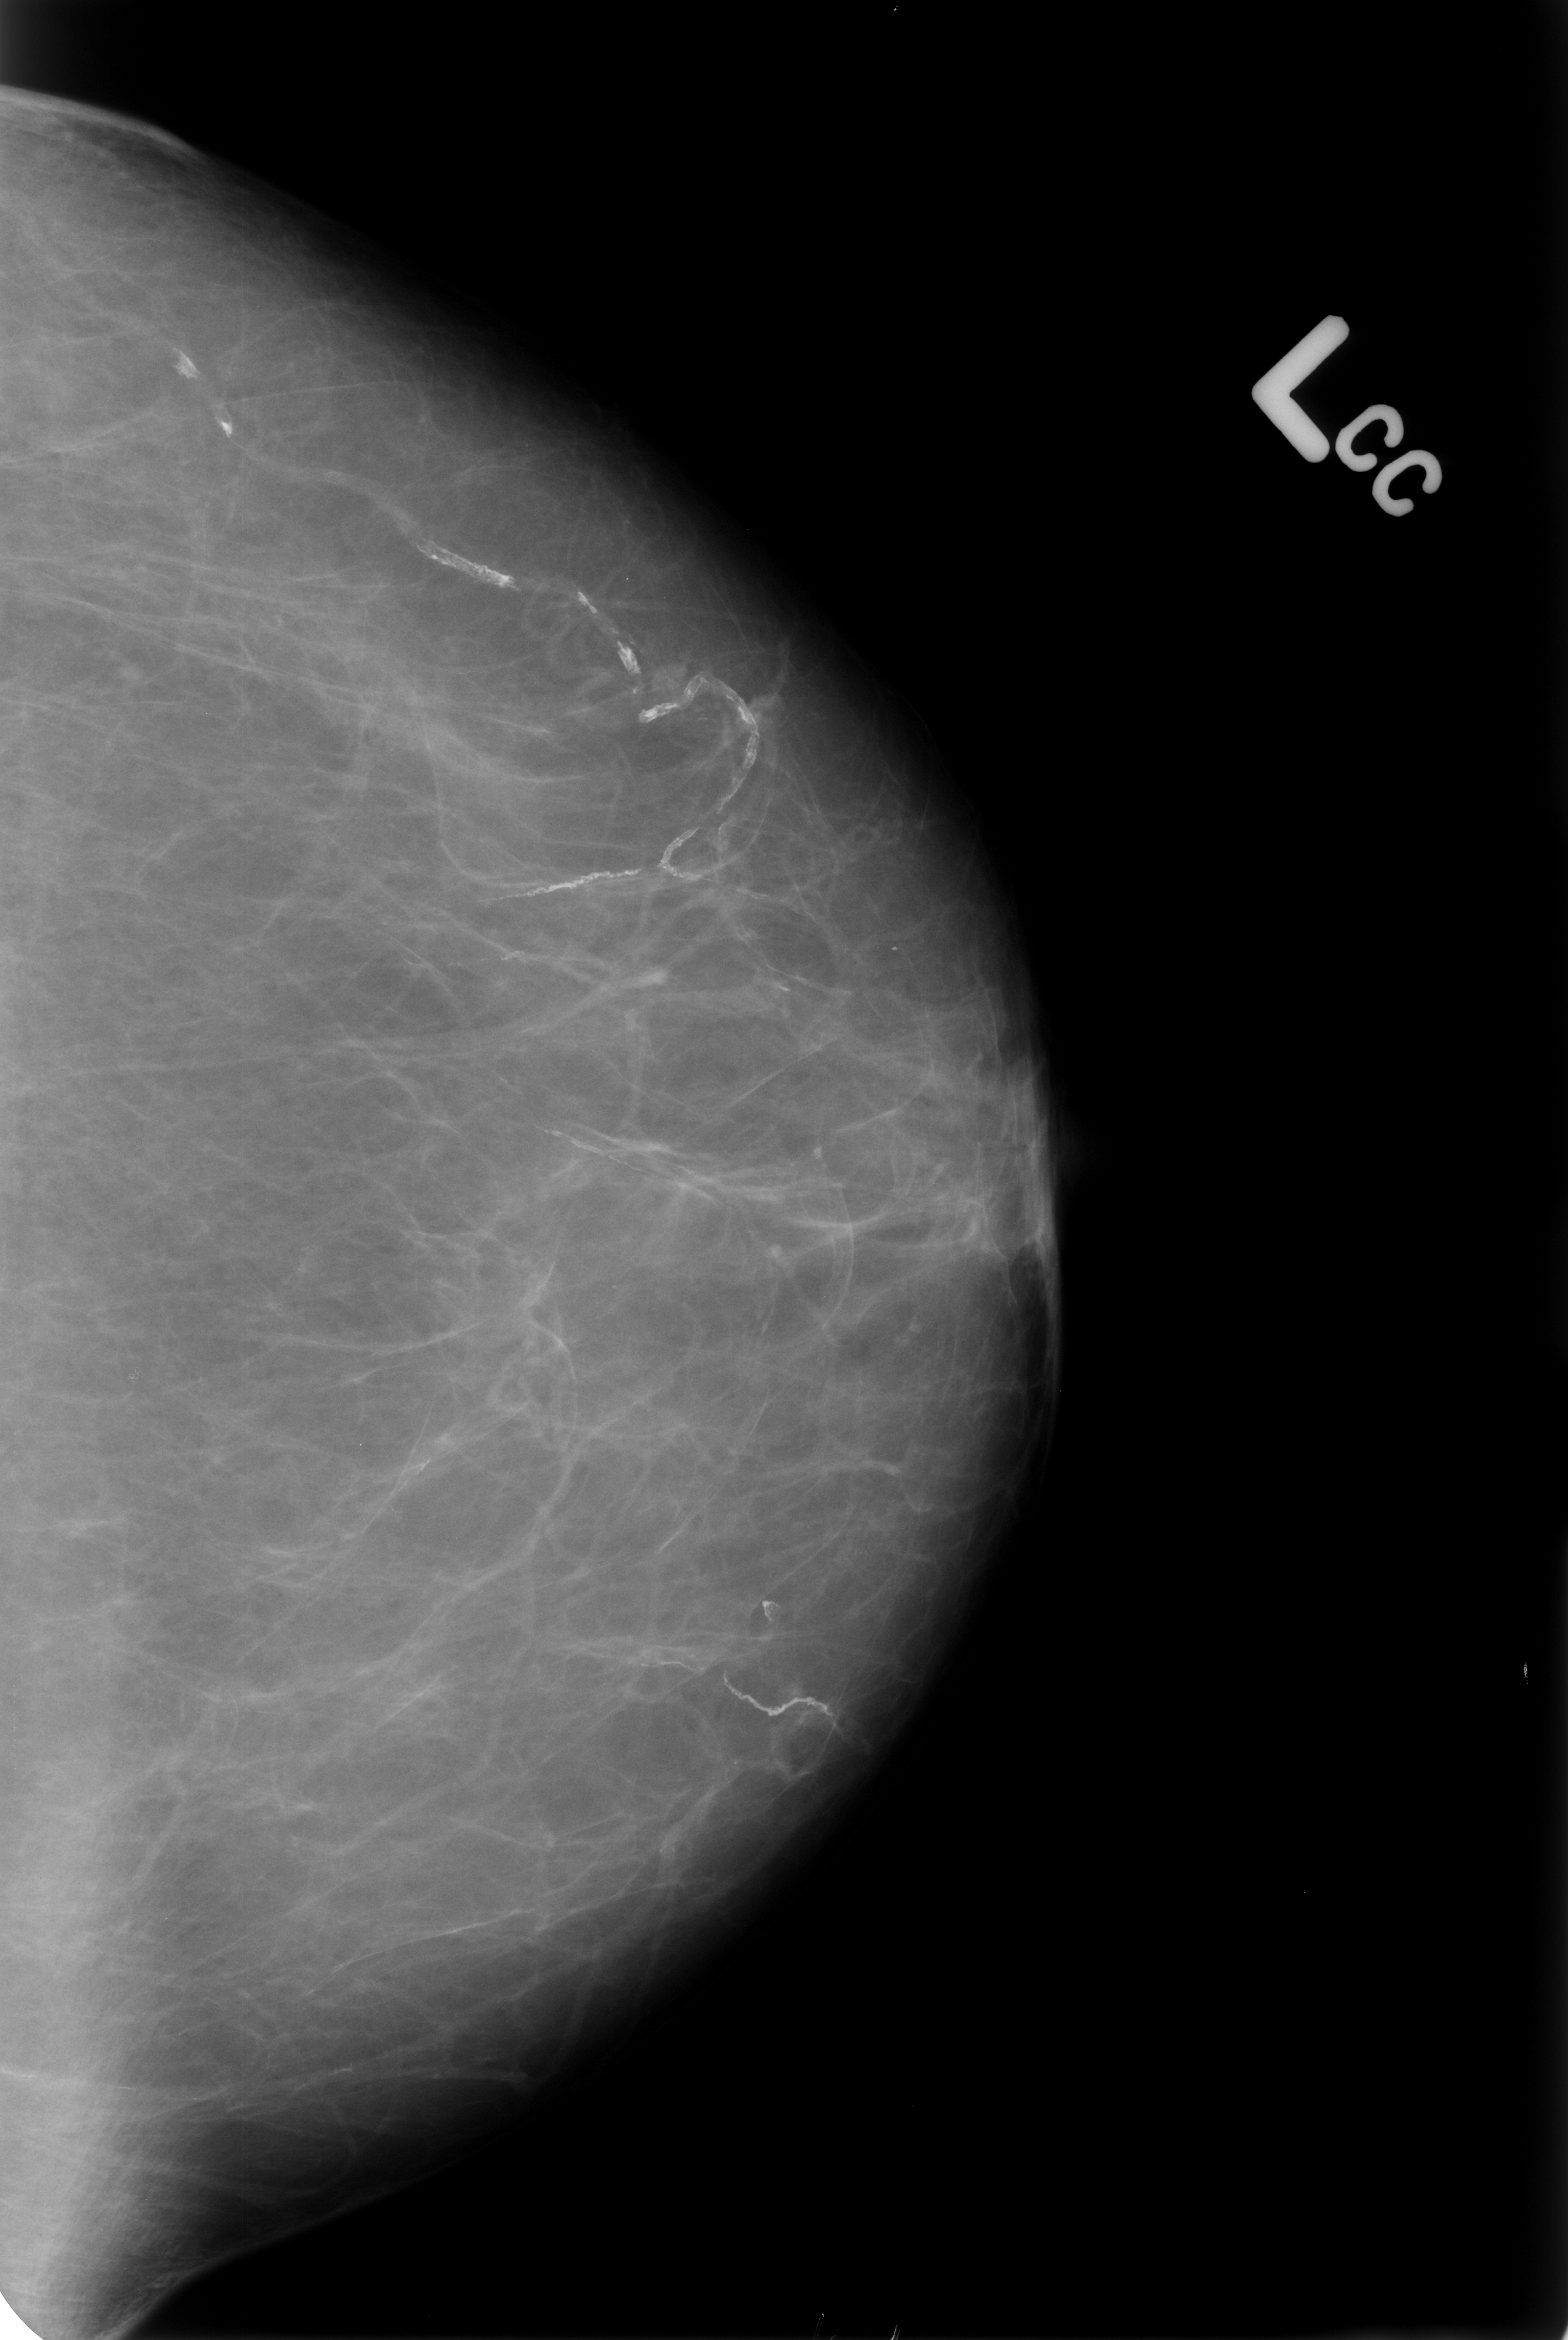
Scanned film-screen mammogram; left breast; CC view; breast composition: almost entirely fatty (BI-RADS density category 1 of 4).
- Marked findings (only marked abnormalities are described; nothing is implied about the rest of the image): Finding 1 of 2: calcifications, morphology vascular; BI-RADS assessment category 2; subtlety rating 5 on a 1 (subtle) to 5 (obvious) scale; benign; no additional work-up was recommended (benign without callback).
- Finding 2 of 2: calcifications, morphology vascular; BI-RADS assessment category 2; subtlety rating 5 on a 1 (subtle) to 5 (obvious) scale; benign; no additional work-up was recommended (benign without callback).